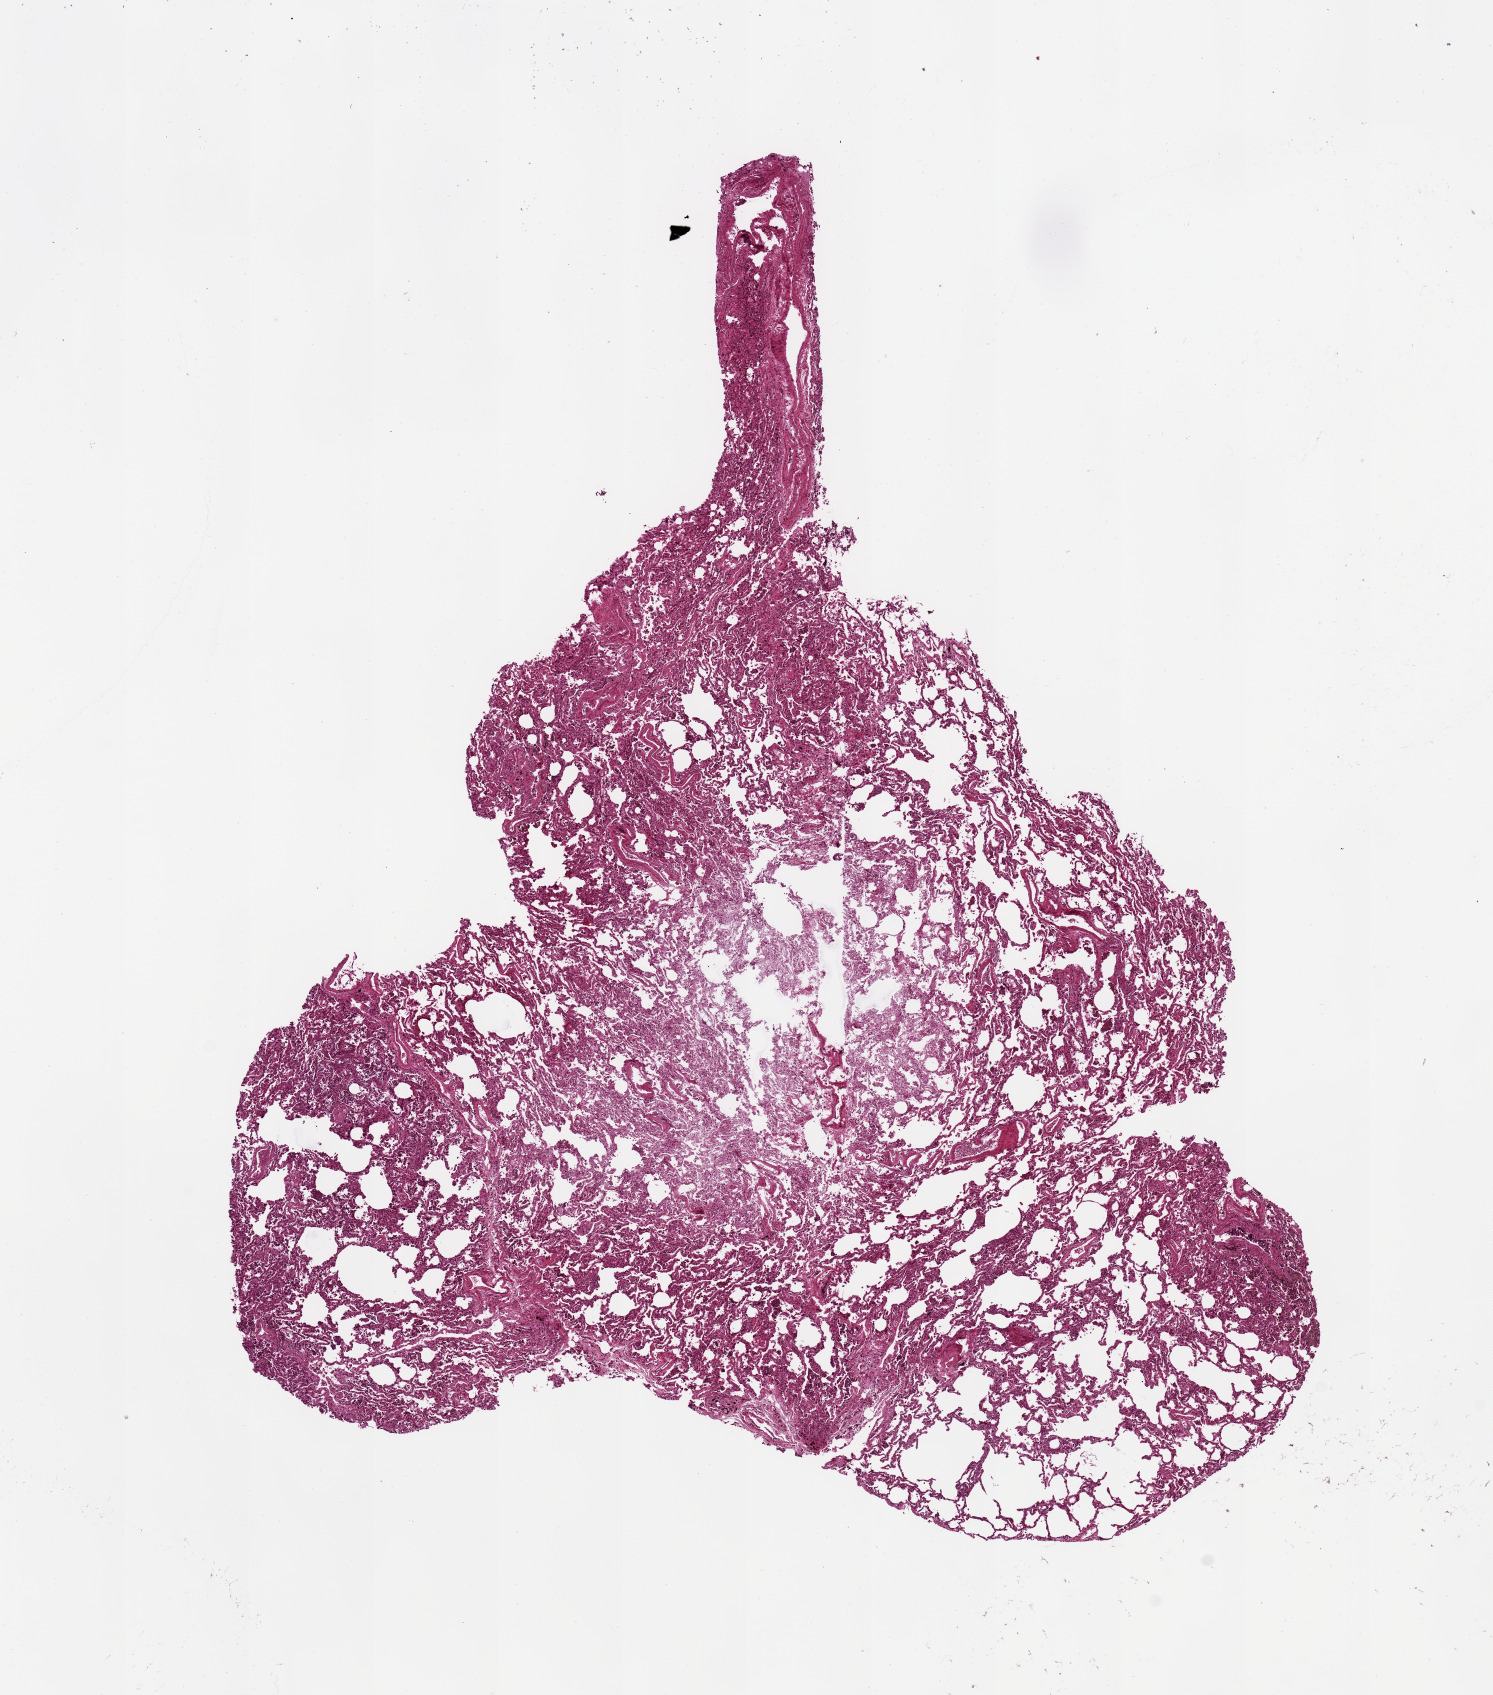
Digitized H&E-stained section, shown as a low-resolution overview of the whole scanned area (about 11.8 x 13.4 mm, slide scanned at 20x); PAXgene-fixed, paraffin-embedded tissue; sampled site (target tissue): lung; donor tissue sample. Male donor.
Review note (as recorded): 9x8mm. Patchy chronic vascular congestion with foci of hemosiderin-laden macrophages.